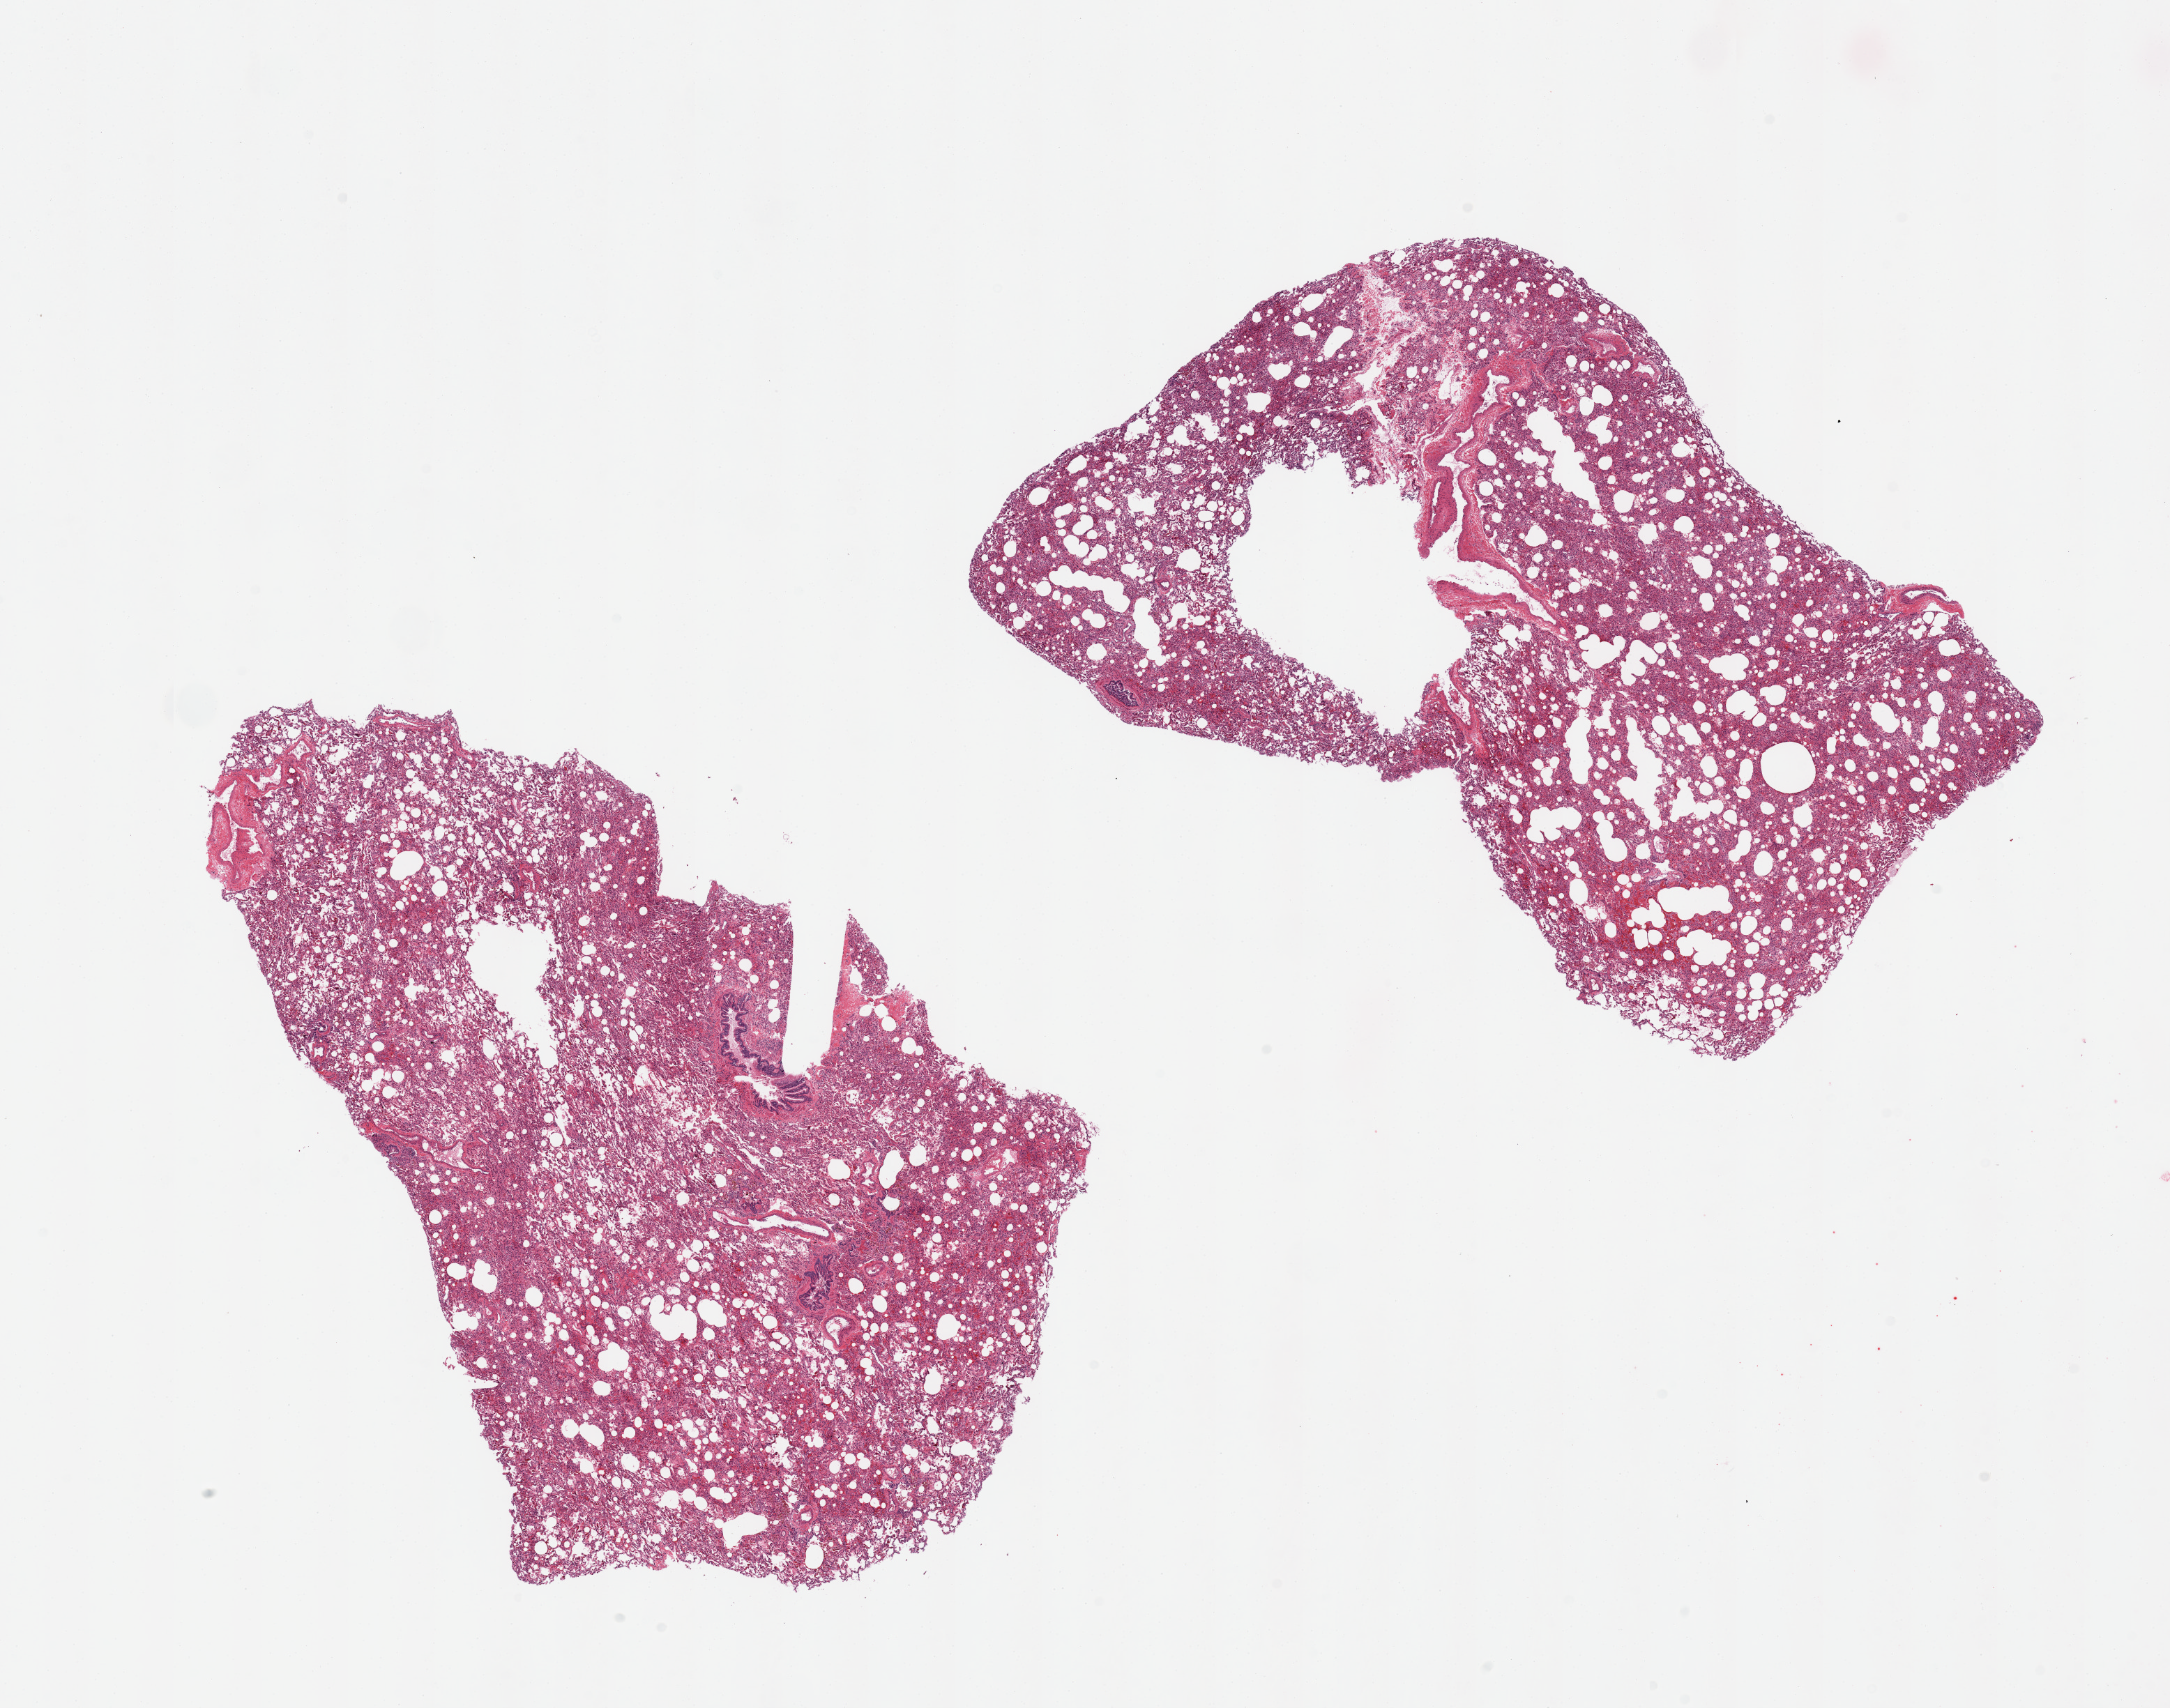
H&E whole-slide image, brightfield — a low-resolution overview of the entire scanned area, about 24.6 x 19.4 mm, PAXgene-fixed paraffin-embedded (PFPE) section, sampled site (target tissue): lung, donor tissue sample. Donor sex: male.
• pathologist's review note for this sample: 2 pieces, congestion, numerous hemosiderin-laden macrophages, atelectasis